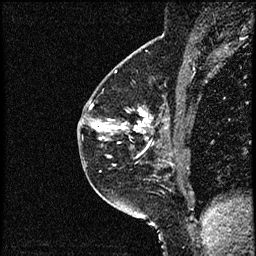
Breast MRI (dynamic contrast-enhanced), one sagittal slice. Slice 36 of 52 in the series (ordered by position). Dynamic contrast-enhanced study with each time point stored as its own series, time point 2 of 3 at this slice position (early post-contrast, ordered by acquisition time). 1.5 T. TE 4.2 ms, TR 17.6 ms. 2 mm slice thickness. 256 × 256 image matrix, field of view 200 × 200 mm. Female patient, age 49 years. Case-level facts recorded for this patient, not image findings: setting: breast cancer imaged before/during neoadjuvant chemotherapy; receptor status: HER2-positive.
Outlined on this slice (semi-automatic segmentation, software-assisted and operator-edited):
- analysis volume of interest (the breast-tissue region the enhancement analysis was run in; not a lesion): box from (x=85, y=65) to (x=182, y=175) px
- tumour enhancement mask (voxels above the 100 % enhancement threshold inside the analysis volume of interest): (x=89, y=105)–(x=153, y=165)